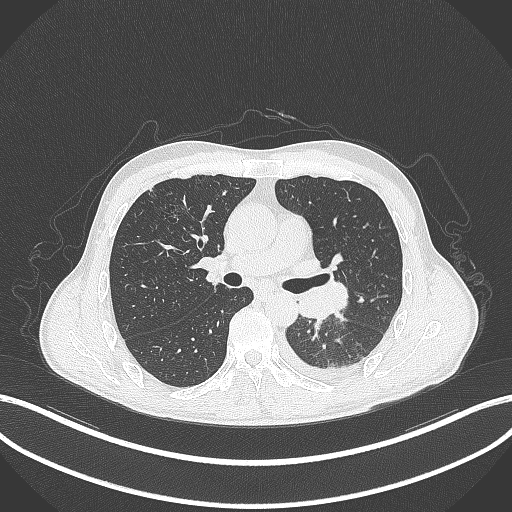
Chest CT, one axial slice. Position 190 of 295 along the scan axis. 120 kVp. Lung window (W 1500 / L -600 HU). 1 mm slice thickness. 512 × 512 image matrix, field of view 400 × 400 mm. Patient: male, 47 years. Case-level facts recorded for this patient, not image findings: clinical TNM (as recorded): T3 N1 M1c; histopathological grade: G3.
Structures marked on this image (rectangle marked by the reading radiologist):
- lung tumour (recorded histology: small cell carcinoma): bounding box [x1, y1, x2, y2] px = [294, 280, 354, 323]